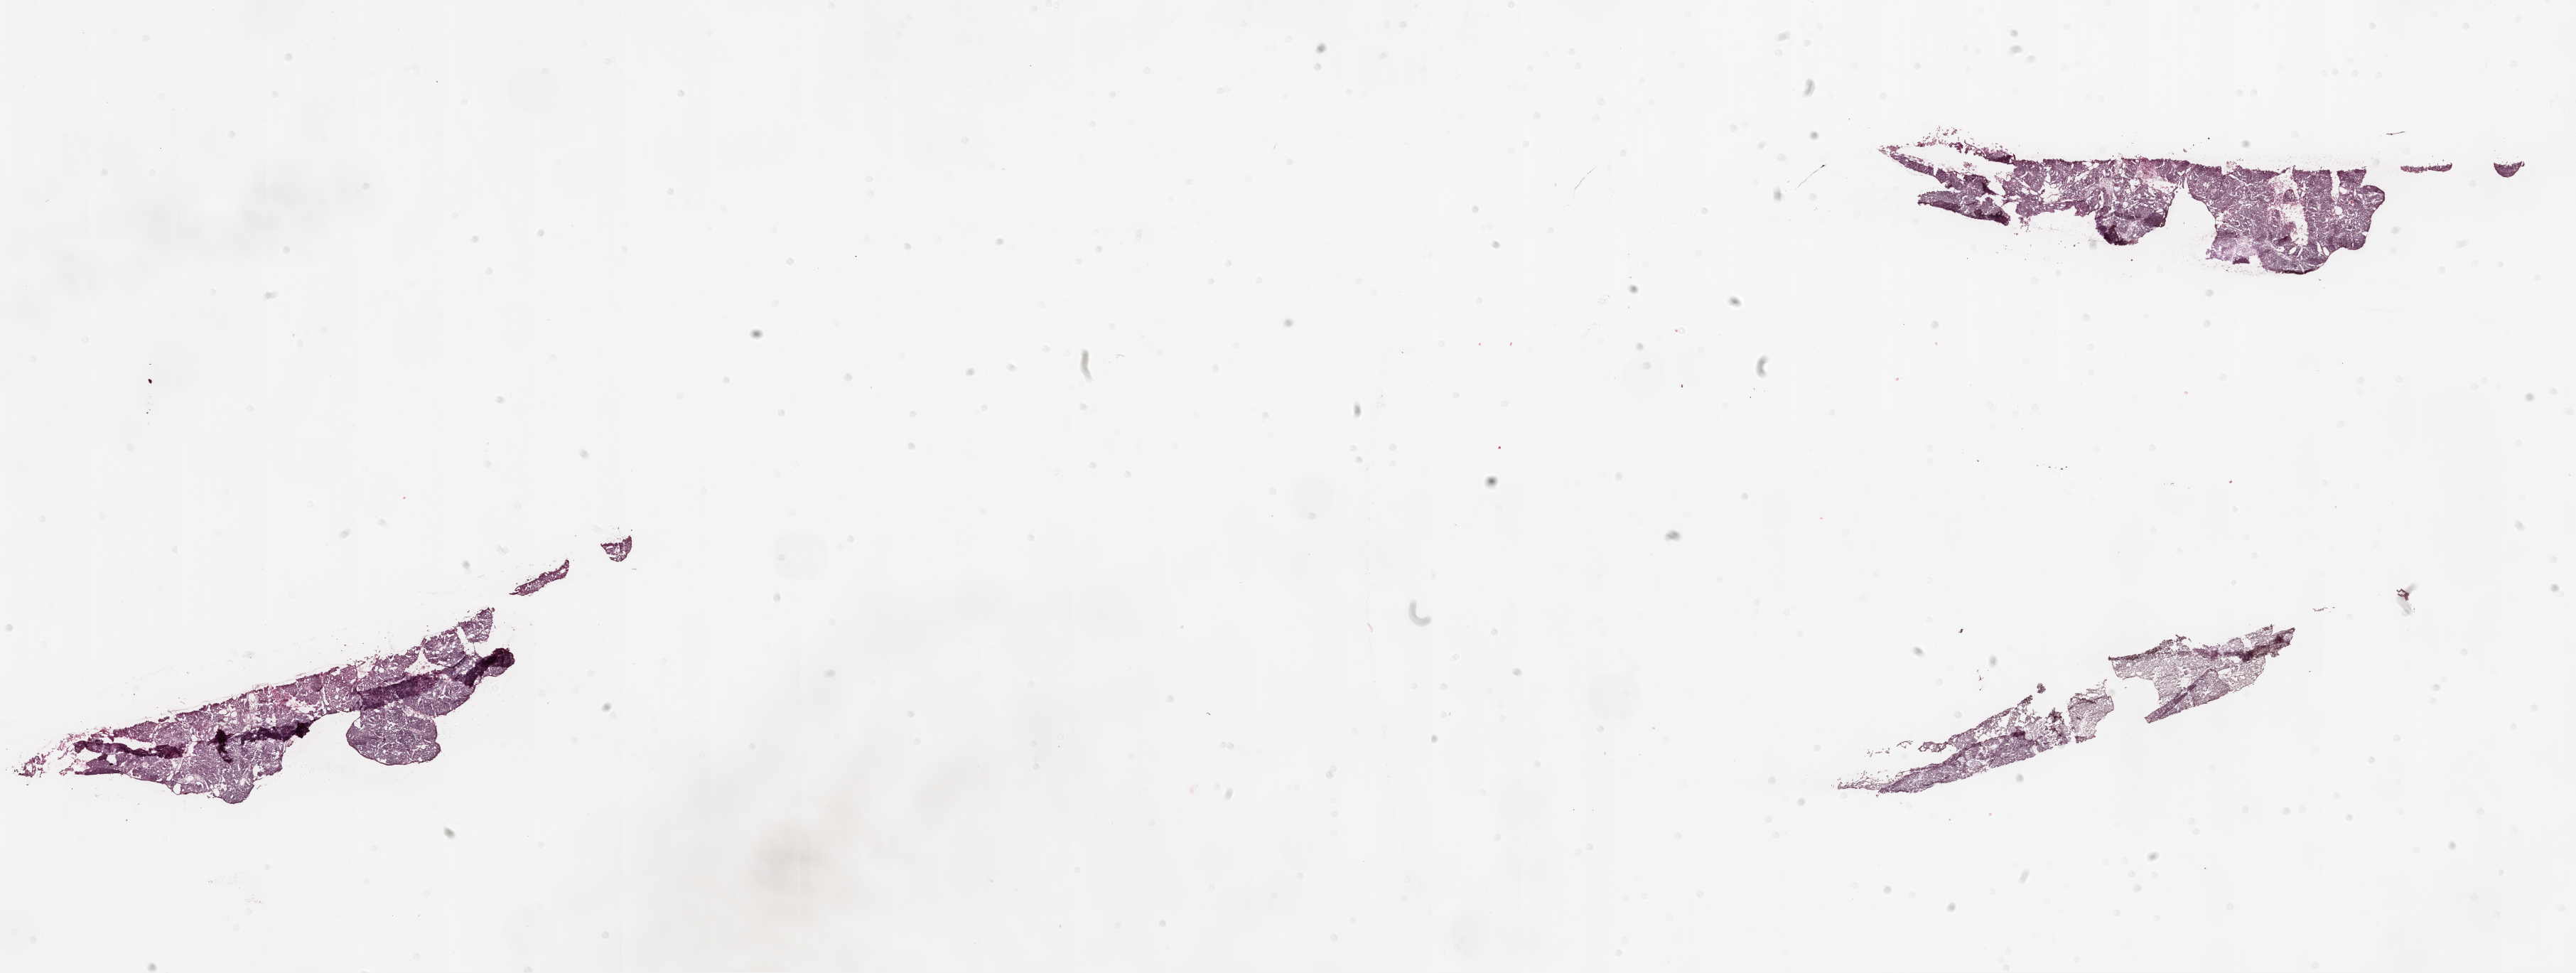
Digitized Hematoxylin and eosin (H&E) stained tissue section (whole slide) — whole scanned area (about 29.1 x 11.0 mm) shown as a low-resolution overview. Frozen section from the top of the tissue portion. Sample: primary tumour, ovary. Female patient; age at initial diagnosis 56 years. Histologic grade: G3 (poorly differentiated). Pathologist review of this section (percent, as recorded): tumour cells 99%, tumour nuclei 99%, normal cells 0%, stromal cells 1%, necrosis 0%.
Laterality: bilateral. Histologic diagnosis: Serous cystadenocarcinoma, NOS. FIGO stage: IIIC.